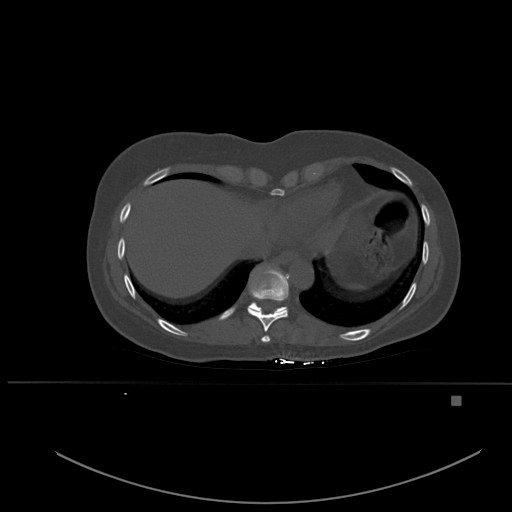
CT including the spine, one axial slice. Position 301 of 651 along the scan axis. Bone window (W 1800 / L 400 HU). 1.5 mm slice thickness. 512 × 512 image matrix, field of view 443 × 443 mm. Patient: female, 49 years. From the clinical record (not read from this slice): primary cancer: breast.
Annotated regions visible in this slice (semi-automatic segmentation, software-assisted and operator-edited):
- T10 vertebra: bounding box (x1, y1, x2, y2) in pixels: (249, 302, 287, 314)
- T8 vertebra: (261, 335, 270, 342)
- T9 vertebra: (247, 269, 290, 332)